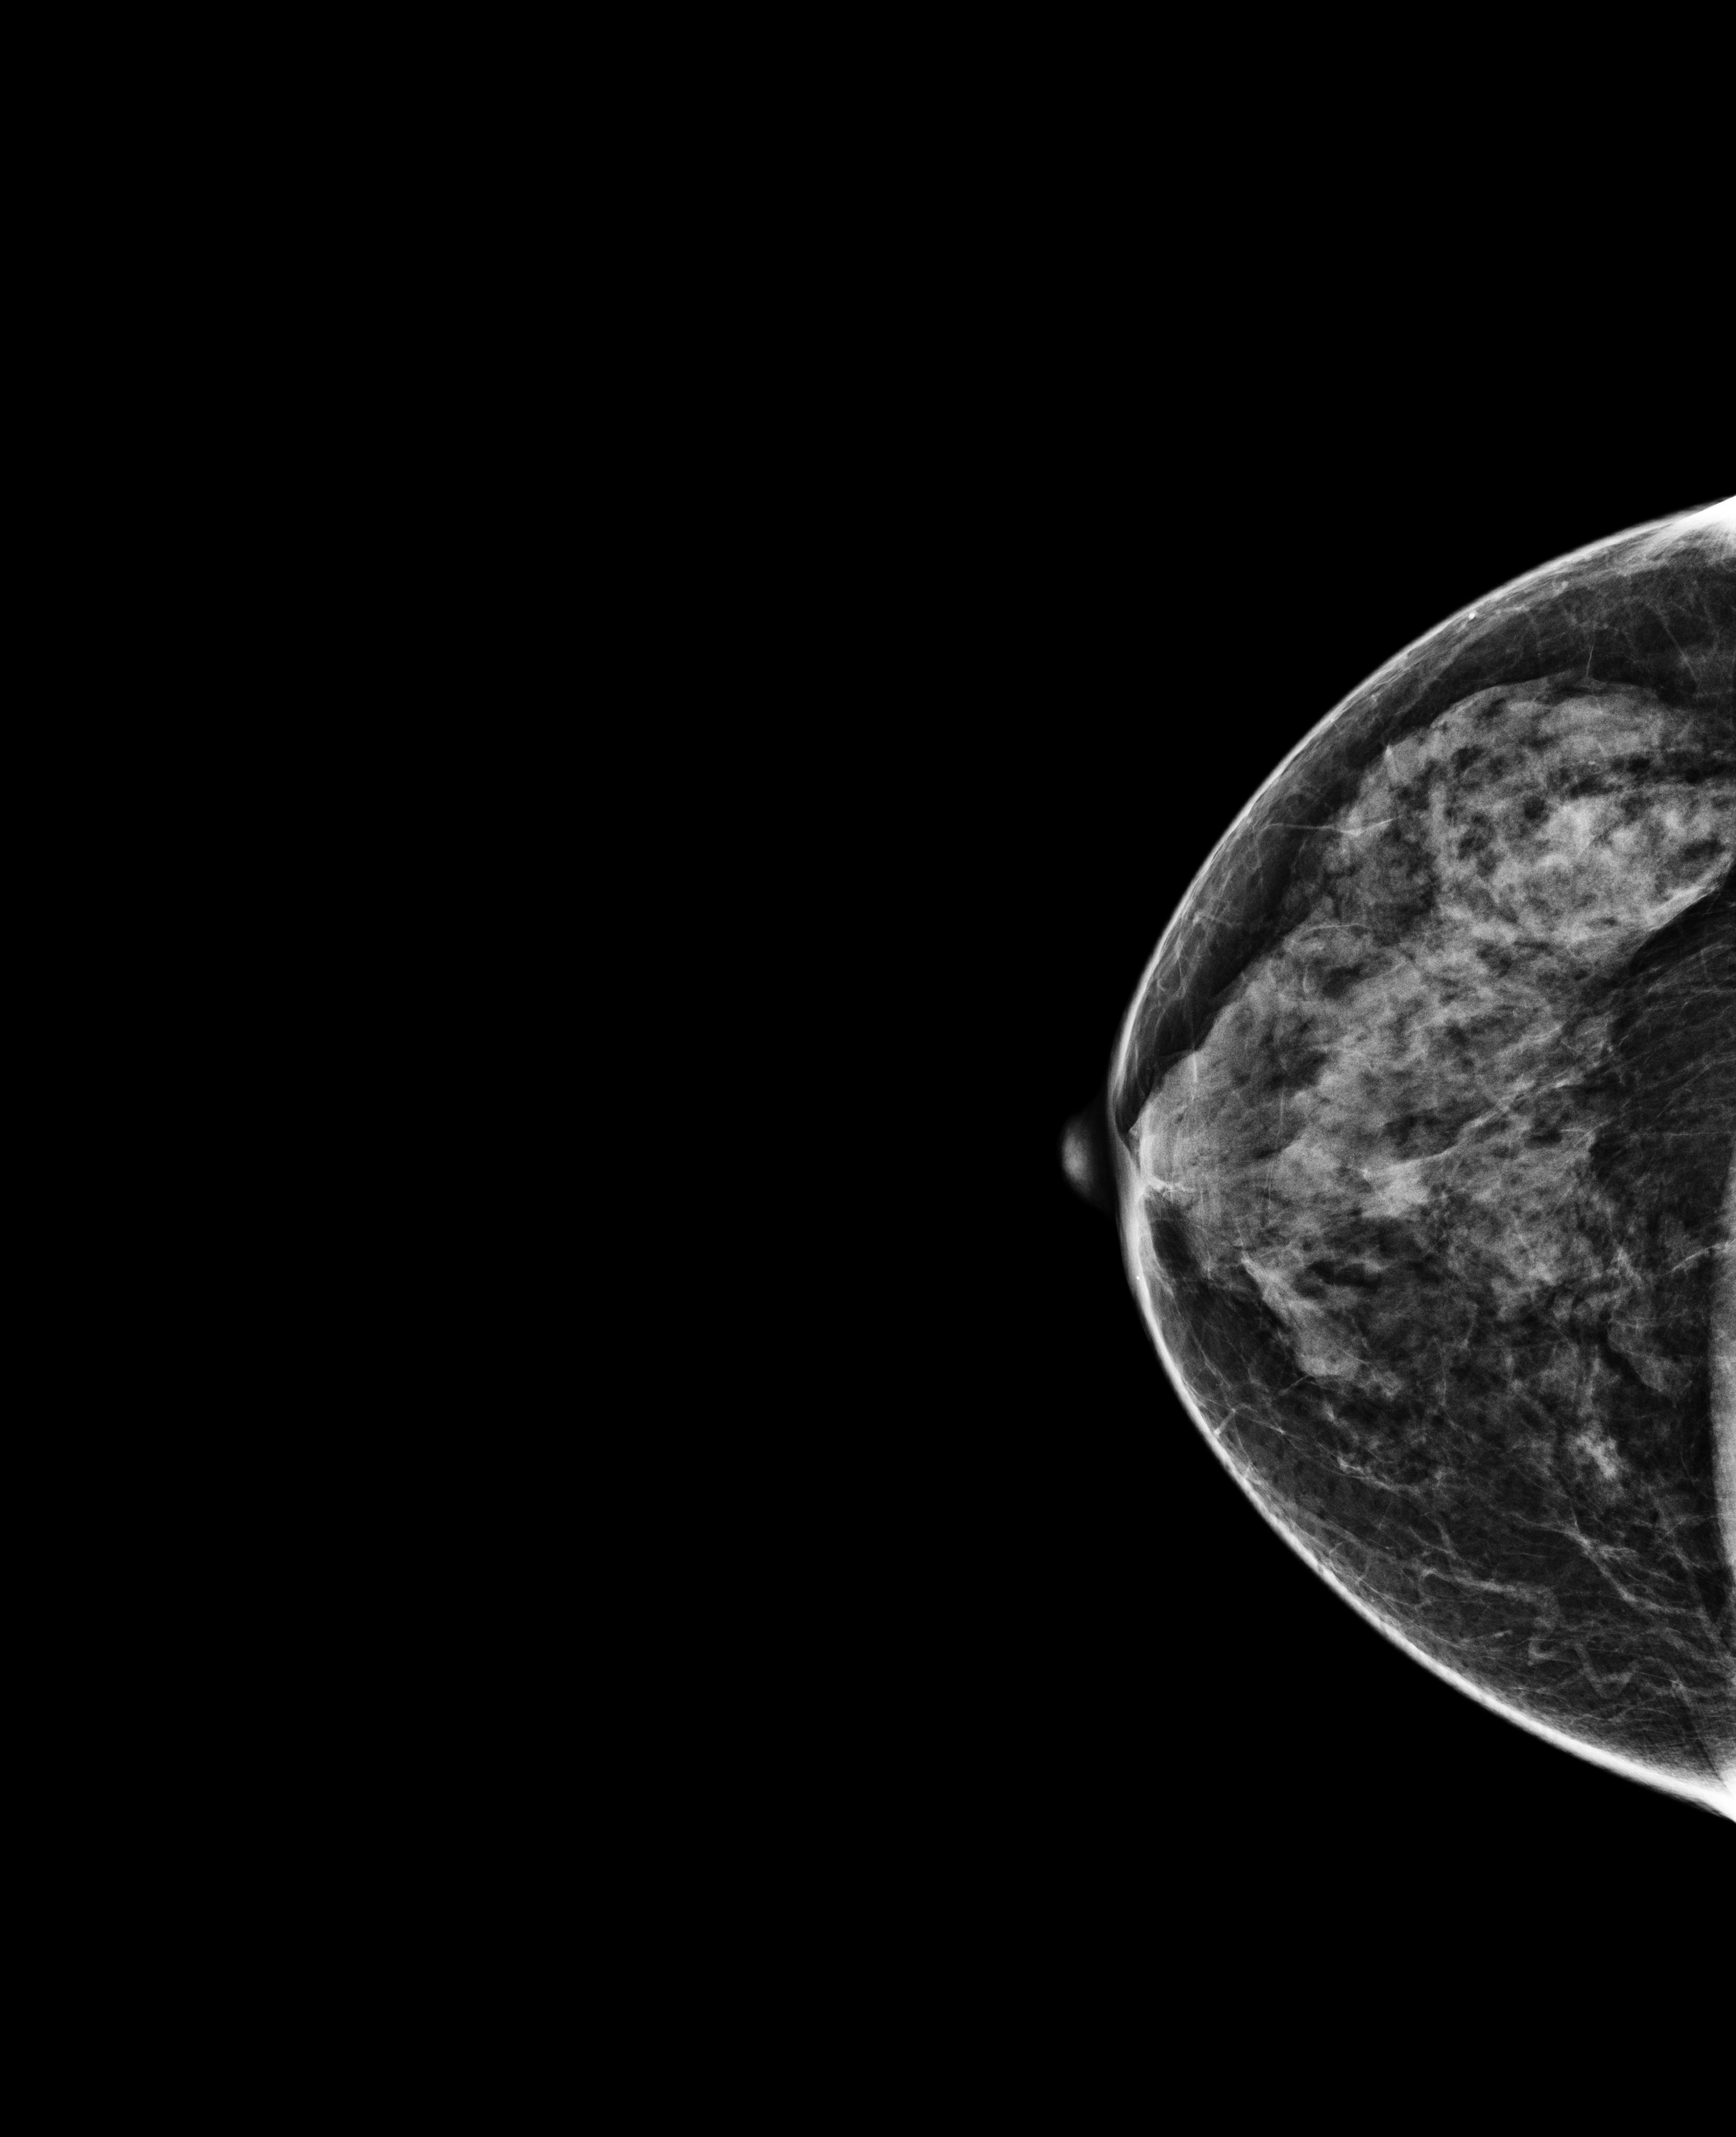
Digital mammogram (FFDM); right breast; craniocaudal (CC) view; screening examination. Patient: female, 66 years.
Breast density at the screening exam (both breasts): heterogeneously dense (BI-RADS density category c). Final BI-RADS assessment for this screening round (tomosynthesis exam, both breasts): category 1. Recall: no recall after this screen.